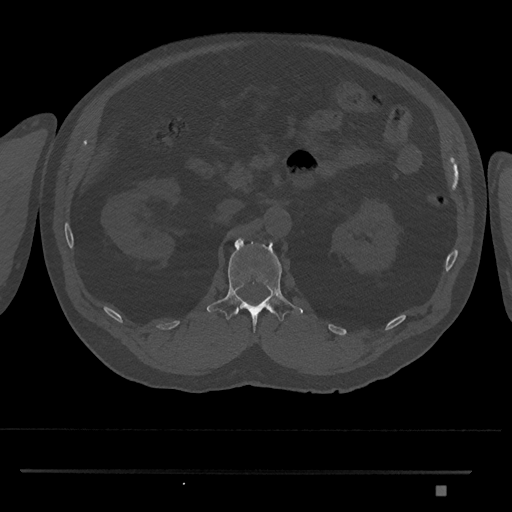
CT including the spine, one axial slice. Reconstruction kernel Br40s/3. 120 kVp. Bone window (W 1800 / L 400 HU). 0.5 mm slice thickness. 512 × 512 image matrix, field of view 429 × 429 mm. Male patient, age 65 years. Case-level facts recorded for this patient, not image findings: primary cancer: prostate.
Annotated regions visible in this slice (semi-automatic segmentation, software-assisted and operator-edited):
- L1 vertebra: box from (x=207, y=238) to (x=303, y=332) px